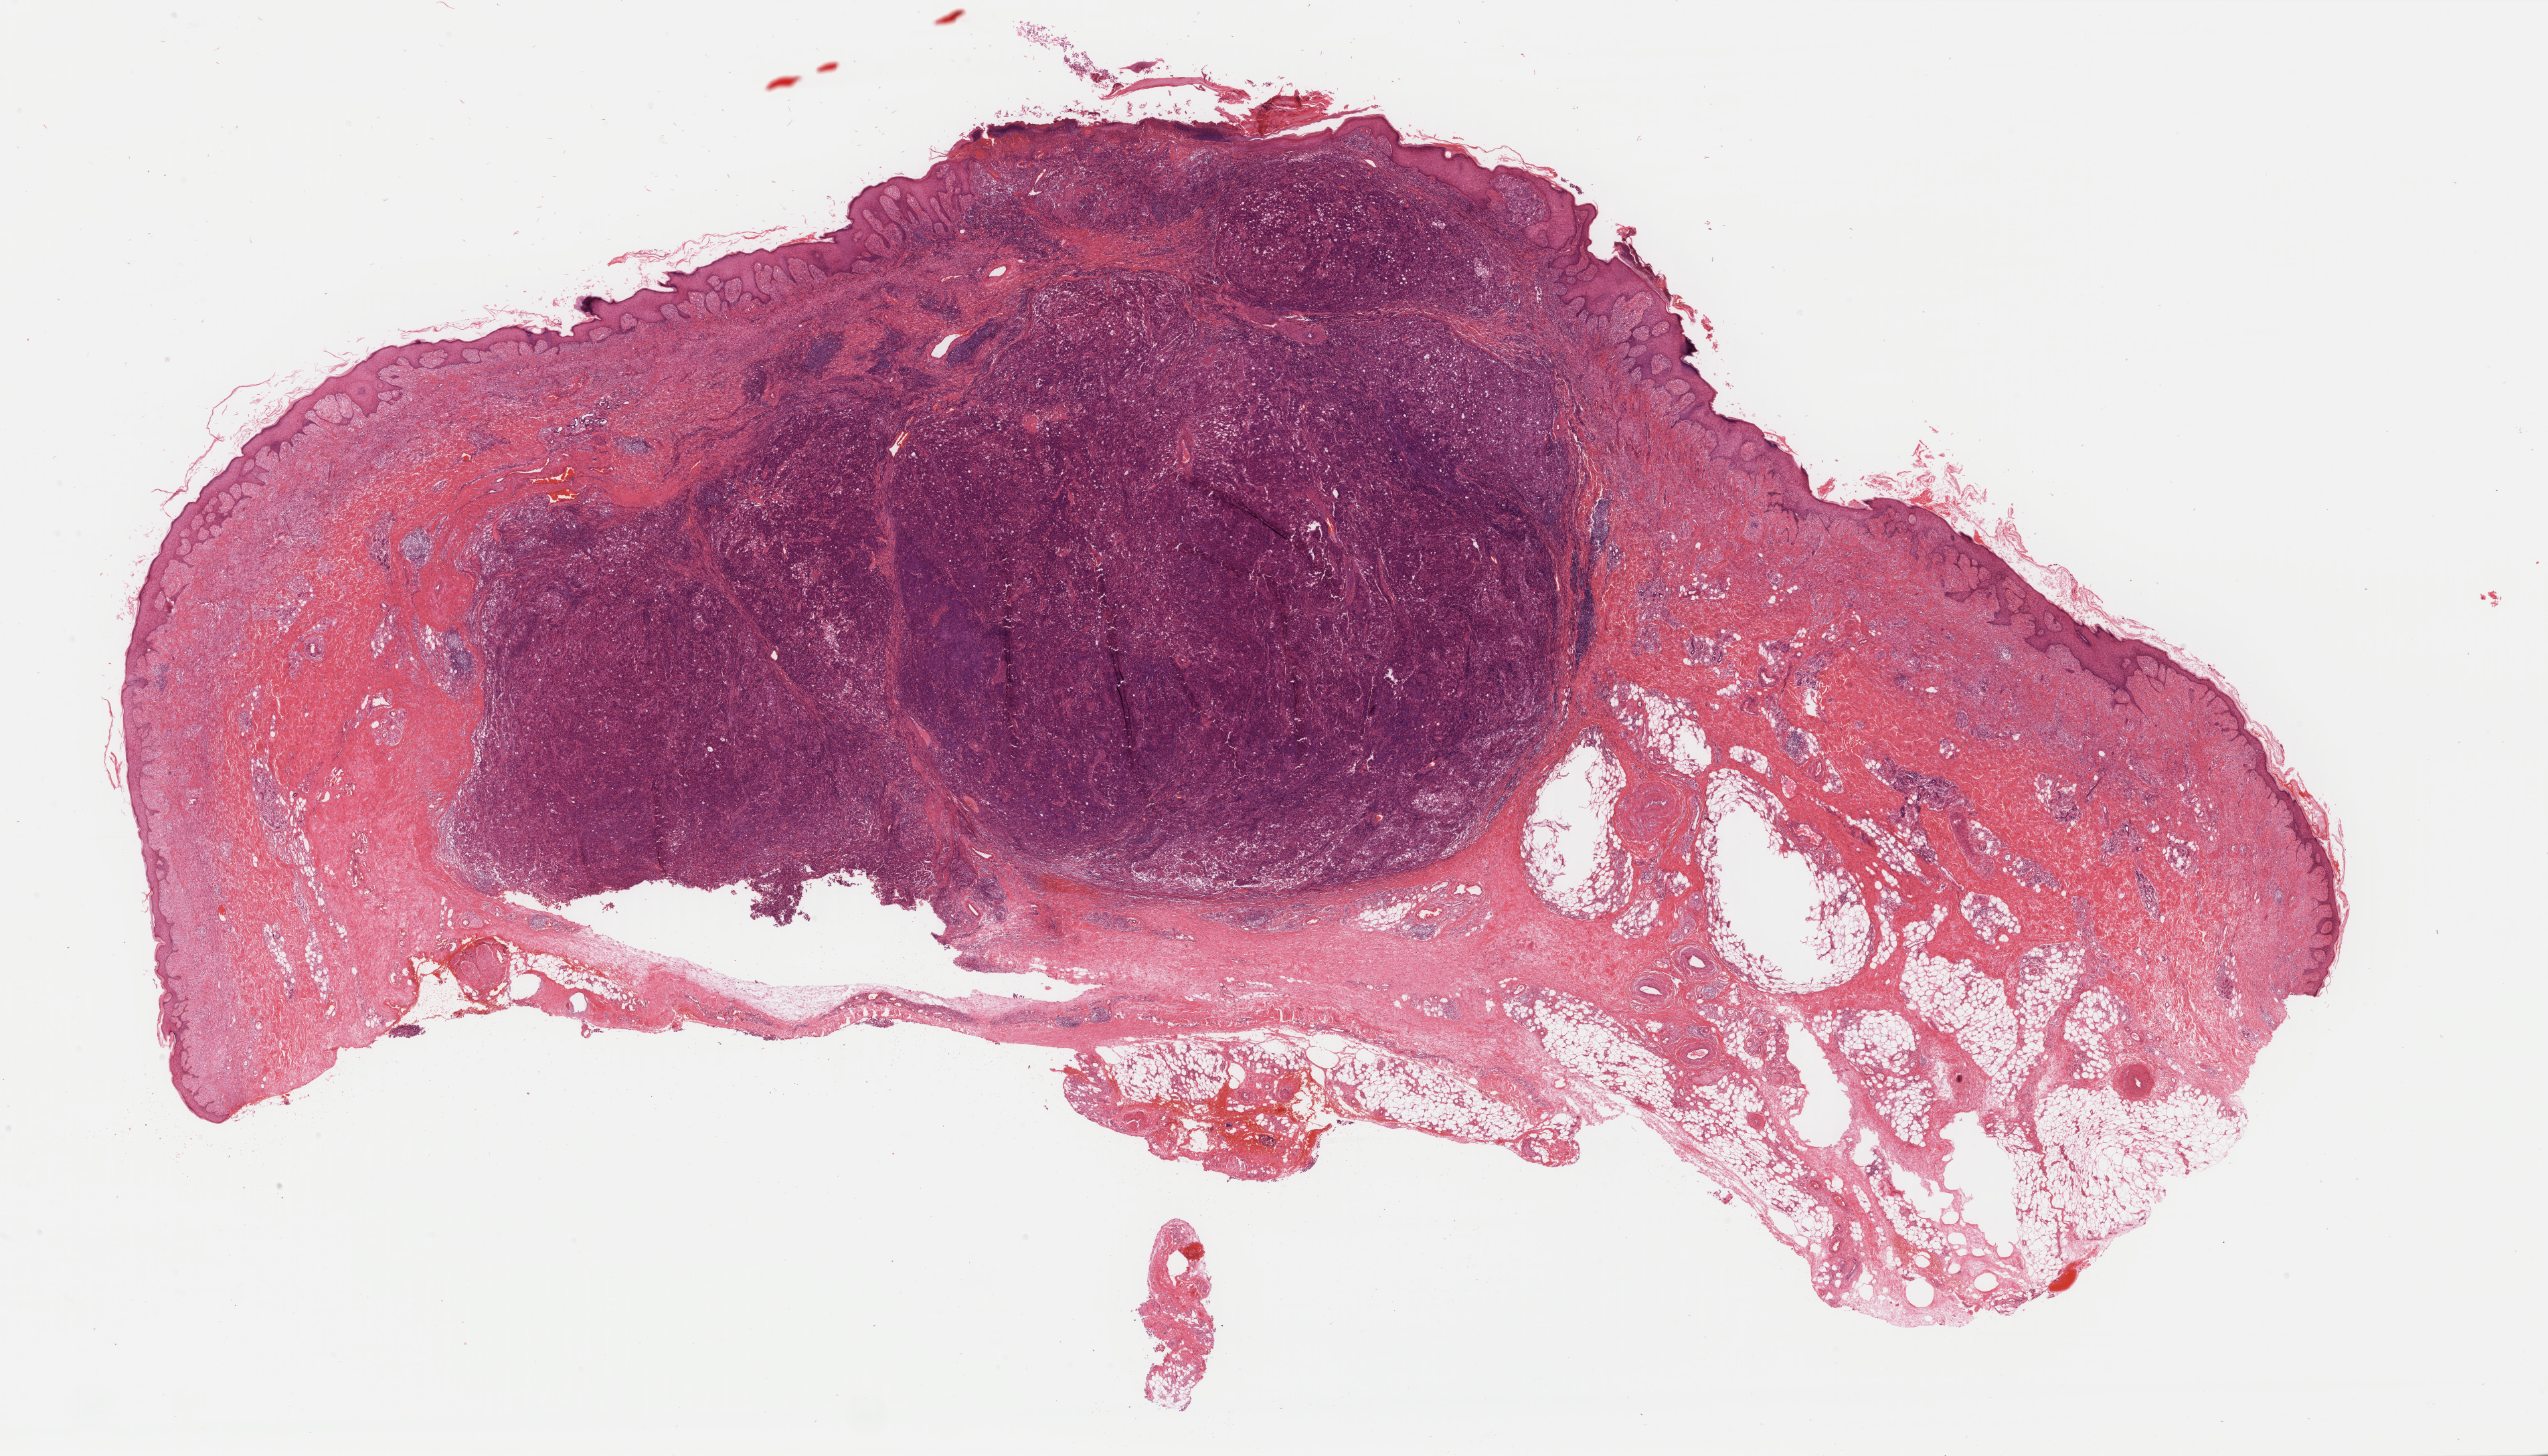
Whole-slide histology image, Hematoxylin and eosin (H&E) stained, a low-resolution overview of the entire scanned area, about 30.2 x 17.3 mm (acquisition: 40x scan). Formalin-fixed paraffin-embedded (FFPE) diagnostic section. Primary tumour sample from the skin. Female, age 78 years at initial diagnosis.
Histologic diagnosis: Amelanotic melanoma. AJCC pathologic stage: IIIC.